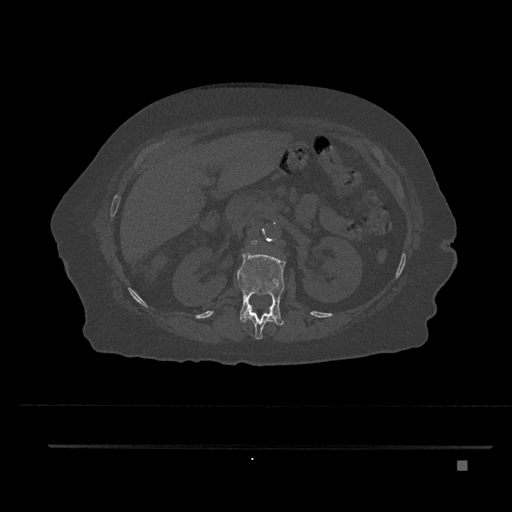
CT including the spine, one axial slice; position 233 of 797 along the scan axis; 120 kVp; bone window (W 1800 / L 400 HU); 0.5 mm slice thickness; 512 × 512 image matrix, field of view 437 × 437 mm. Patient: female, 76 years. Case-level facts recorded for this patient, not image findings: primary cancer: lung; vertebrae with lytic lesions (as recorded): T11, L3.
Outlined on this slice (semi-automatic segmentation, software-assisted and operator-edited):
- L1 vertebra: bounding box <237,250,285,326> (left, top, right, bottom; pixels)
- L2 vertebra: <251,240,258,246>
- T12 vertebra: <244,305,276,340>